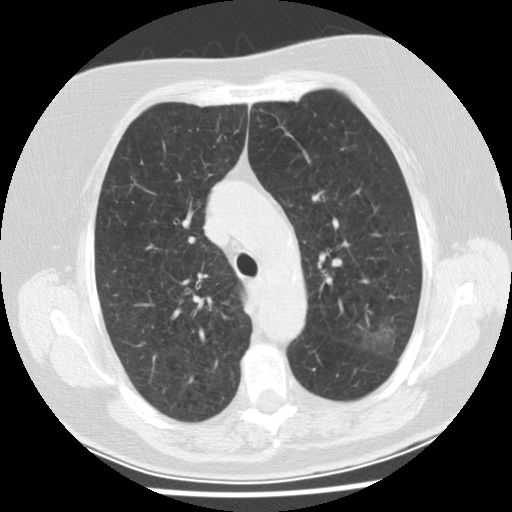
Chest CT (low-dose screening protocol), one axial image; baseline annual screen; lung window (W 1500 / L -600 HU); 2.5 mm slice thickness; slice 112 of 149 in the series. Female, age 74 years at enrolment. Former smoker at enrolment.
Lesion marked by an expert reader, box from (x=337, y=308) to (x=408, y=364) px. The screening reader recorded 2 non-calcified nodules or masses ≥4 mm on this exam (left upper lobe, left lower lobe); which of them this box marks is not recorded. Official screen result: positive, change unspecified: nodule(s) >= 4 mm or enlarging nodule(s), mass(es), or other non-specific abnormalities suspicious for lung cancer.